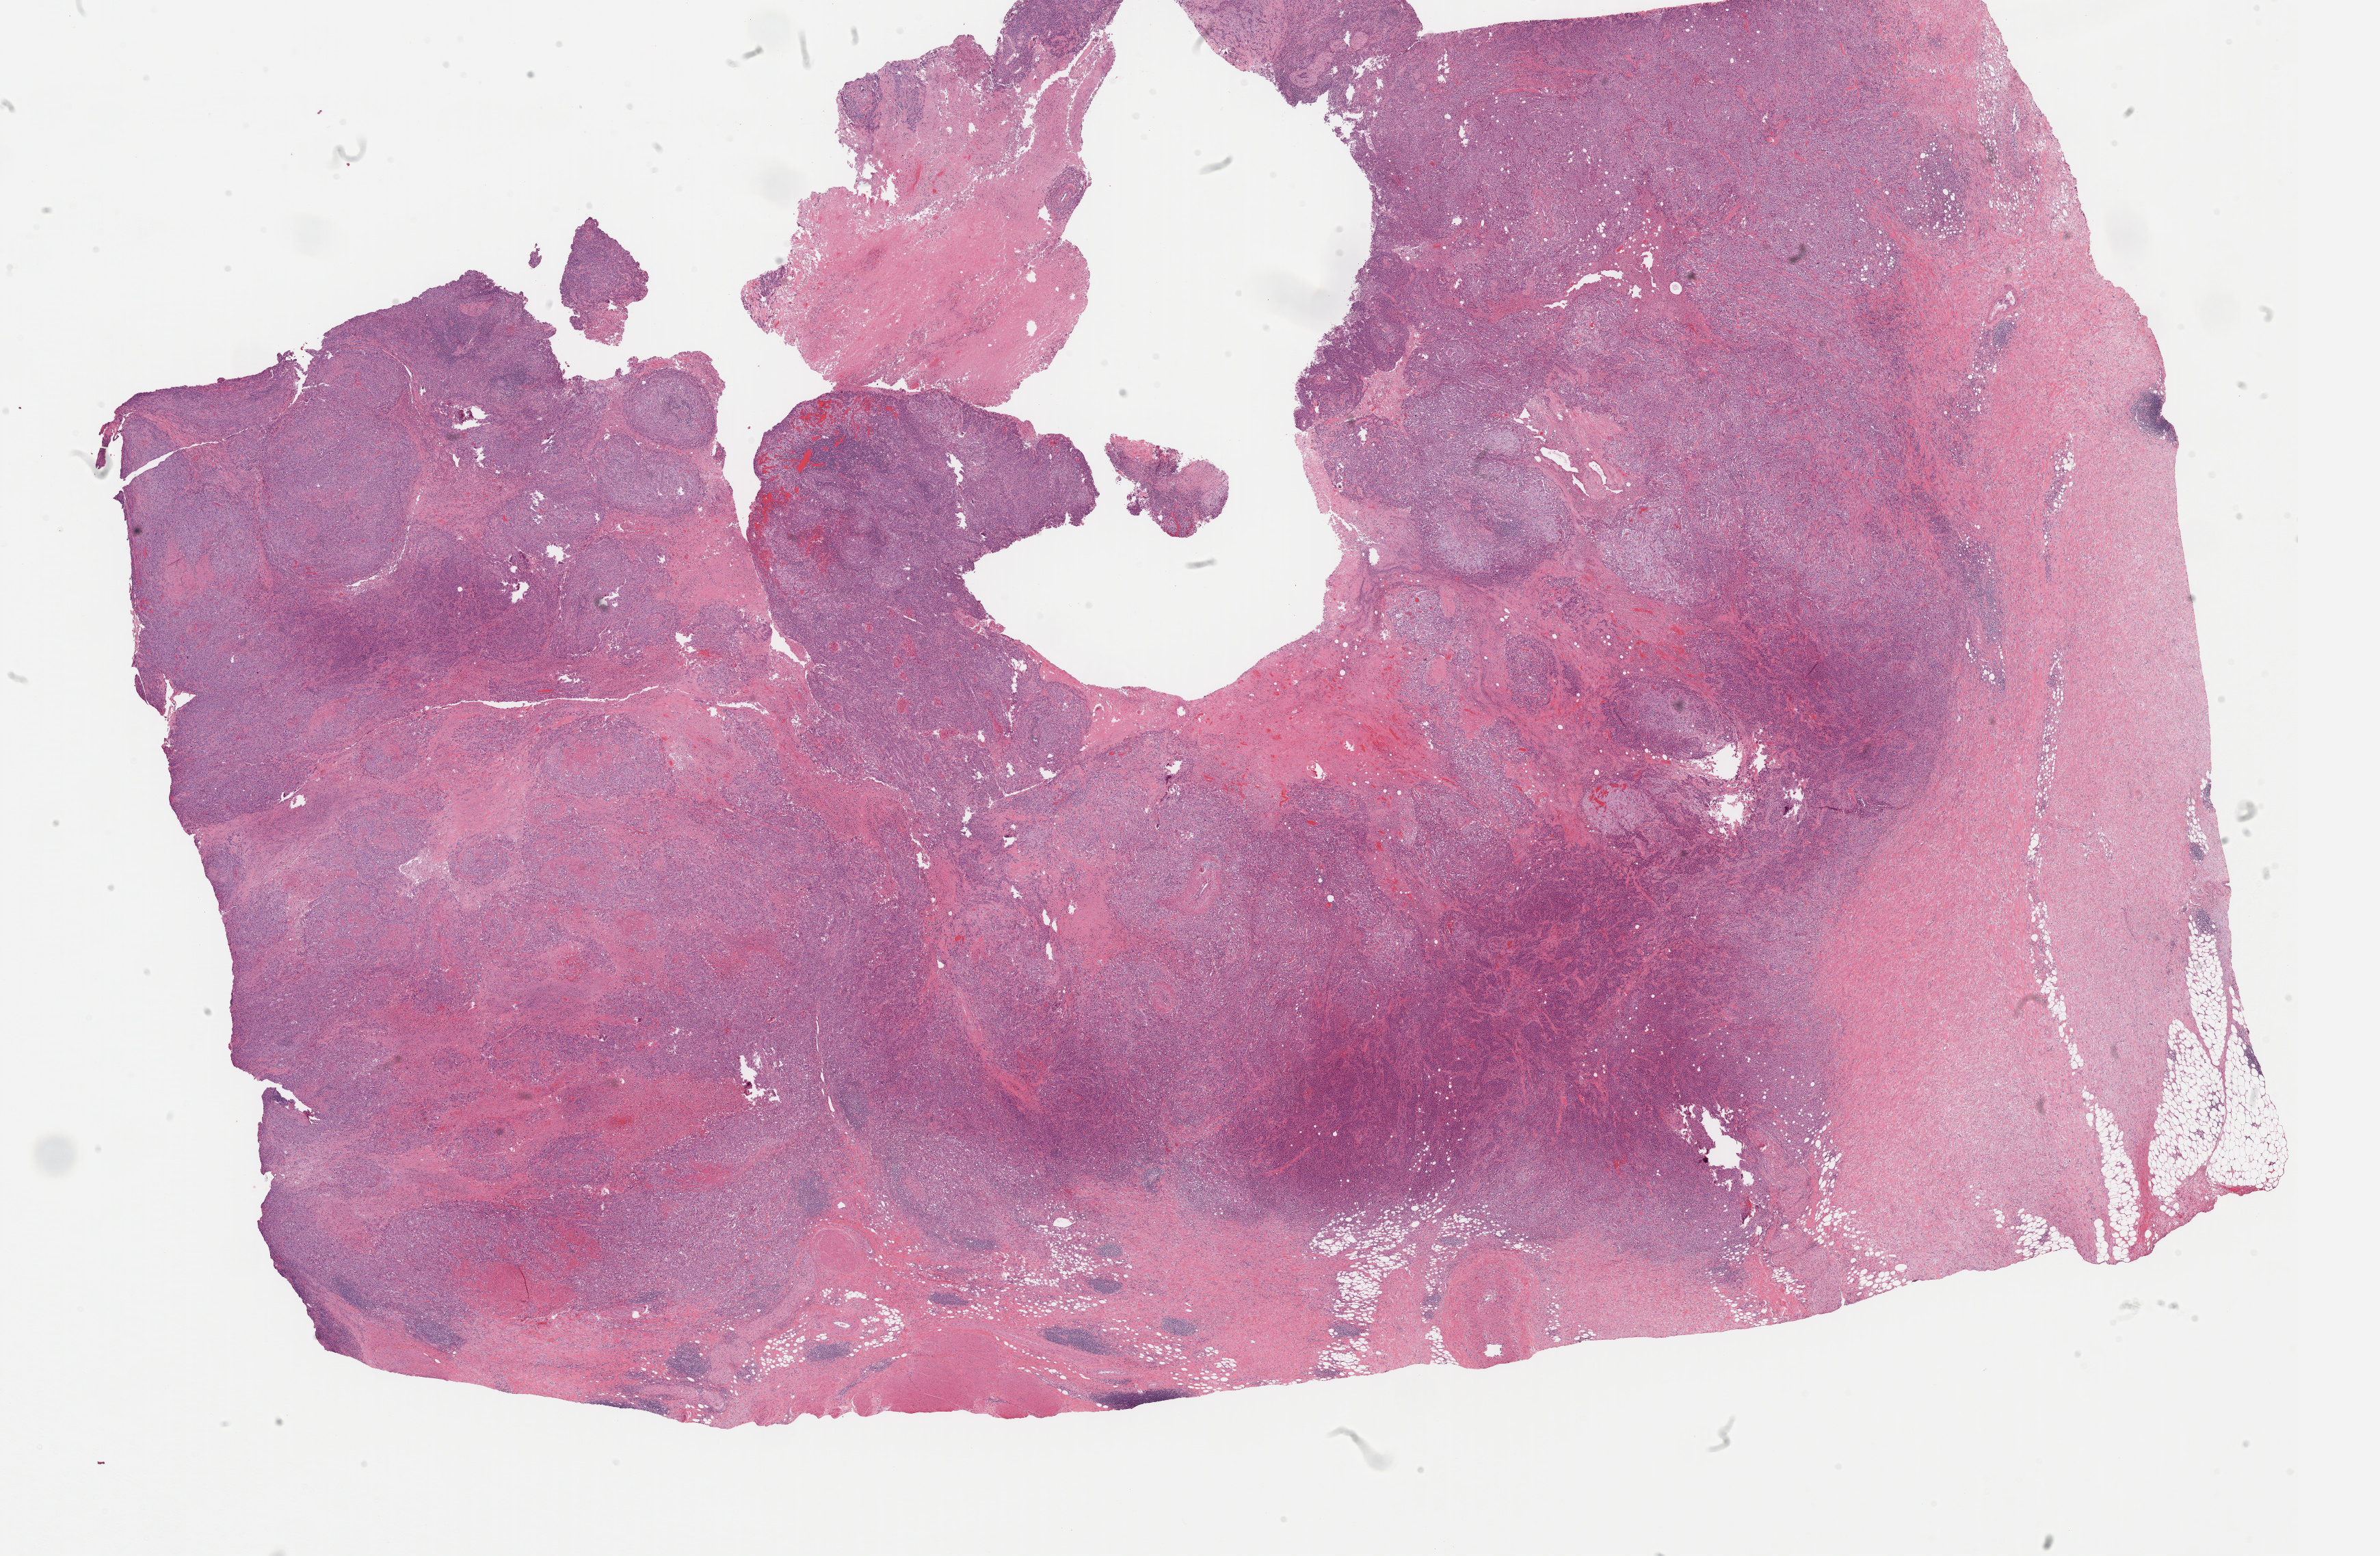
Digitized H&E-stained tissue section (whole slide) — a low-resolution overview of the entire scanned area, about 27.5 x 17.9 mm, formalin-fixed paraffin-embedded (FFPE) diagnostic section, primary tumour sample from the bladder. Patient: male, age at initial diagnosis 76 years. Histologic grade: high grade.
Pathologic diagnosis: Transitional cell carcinoma (lateral wall of bladder). Lymph nodes positive (case pathology): 0 of 28 examined. TNM: T3b N0 M0. AJCC pathologic stage: III (7th edition).